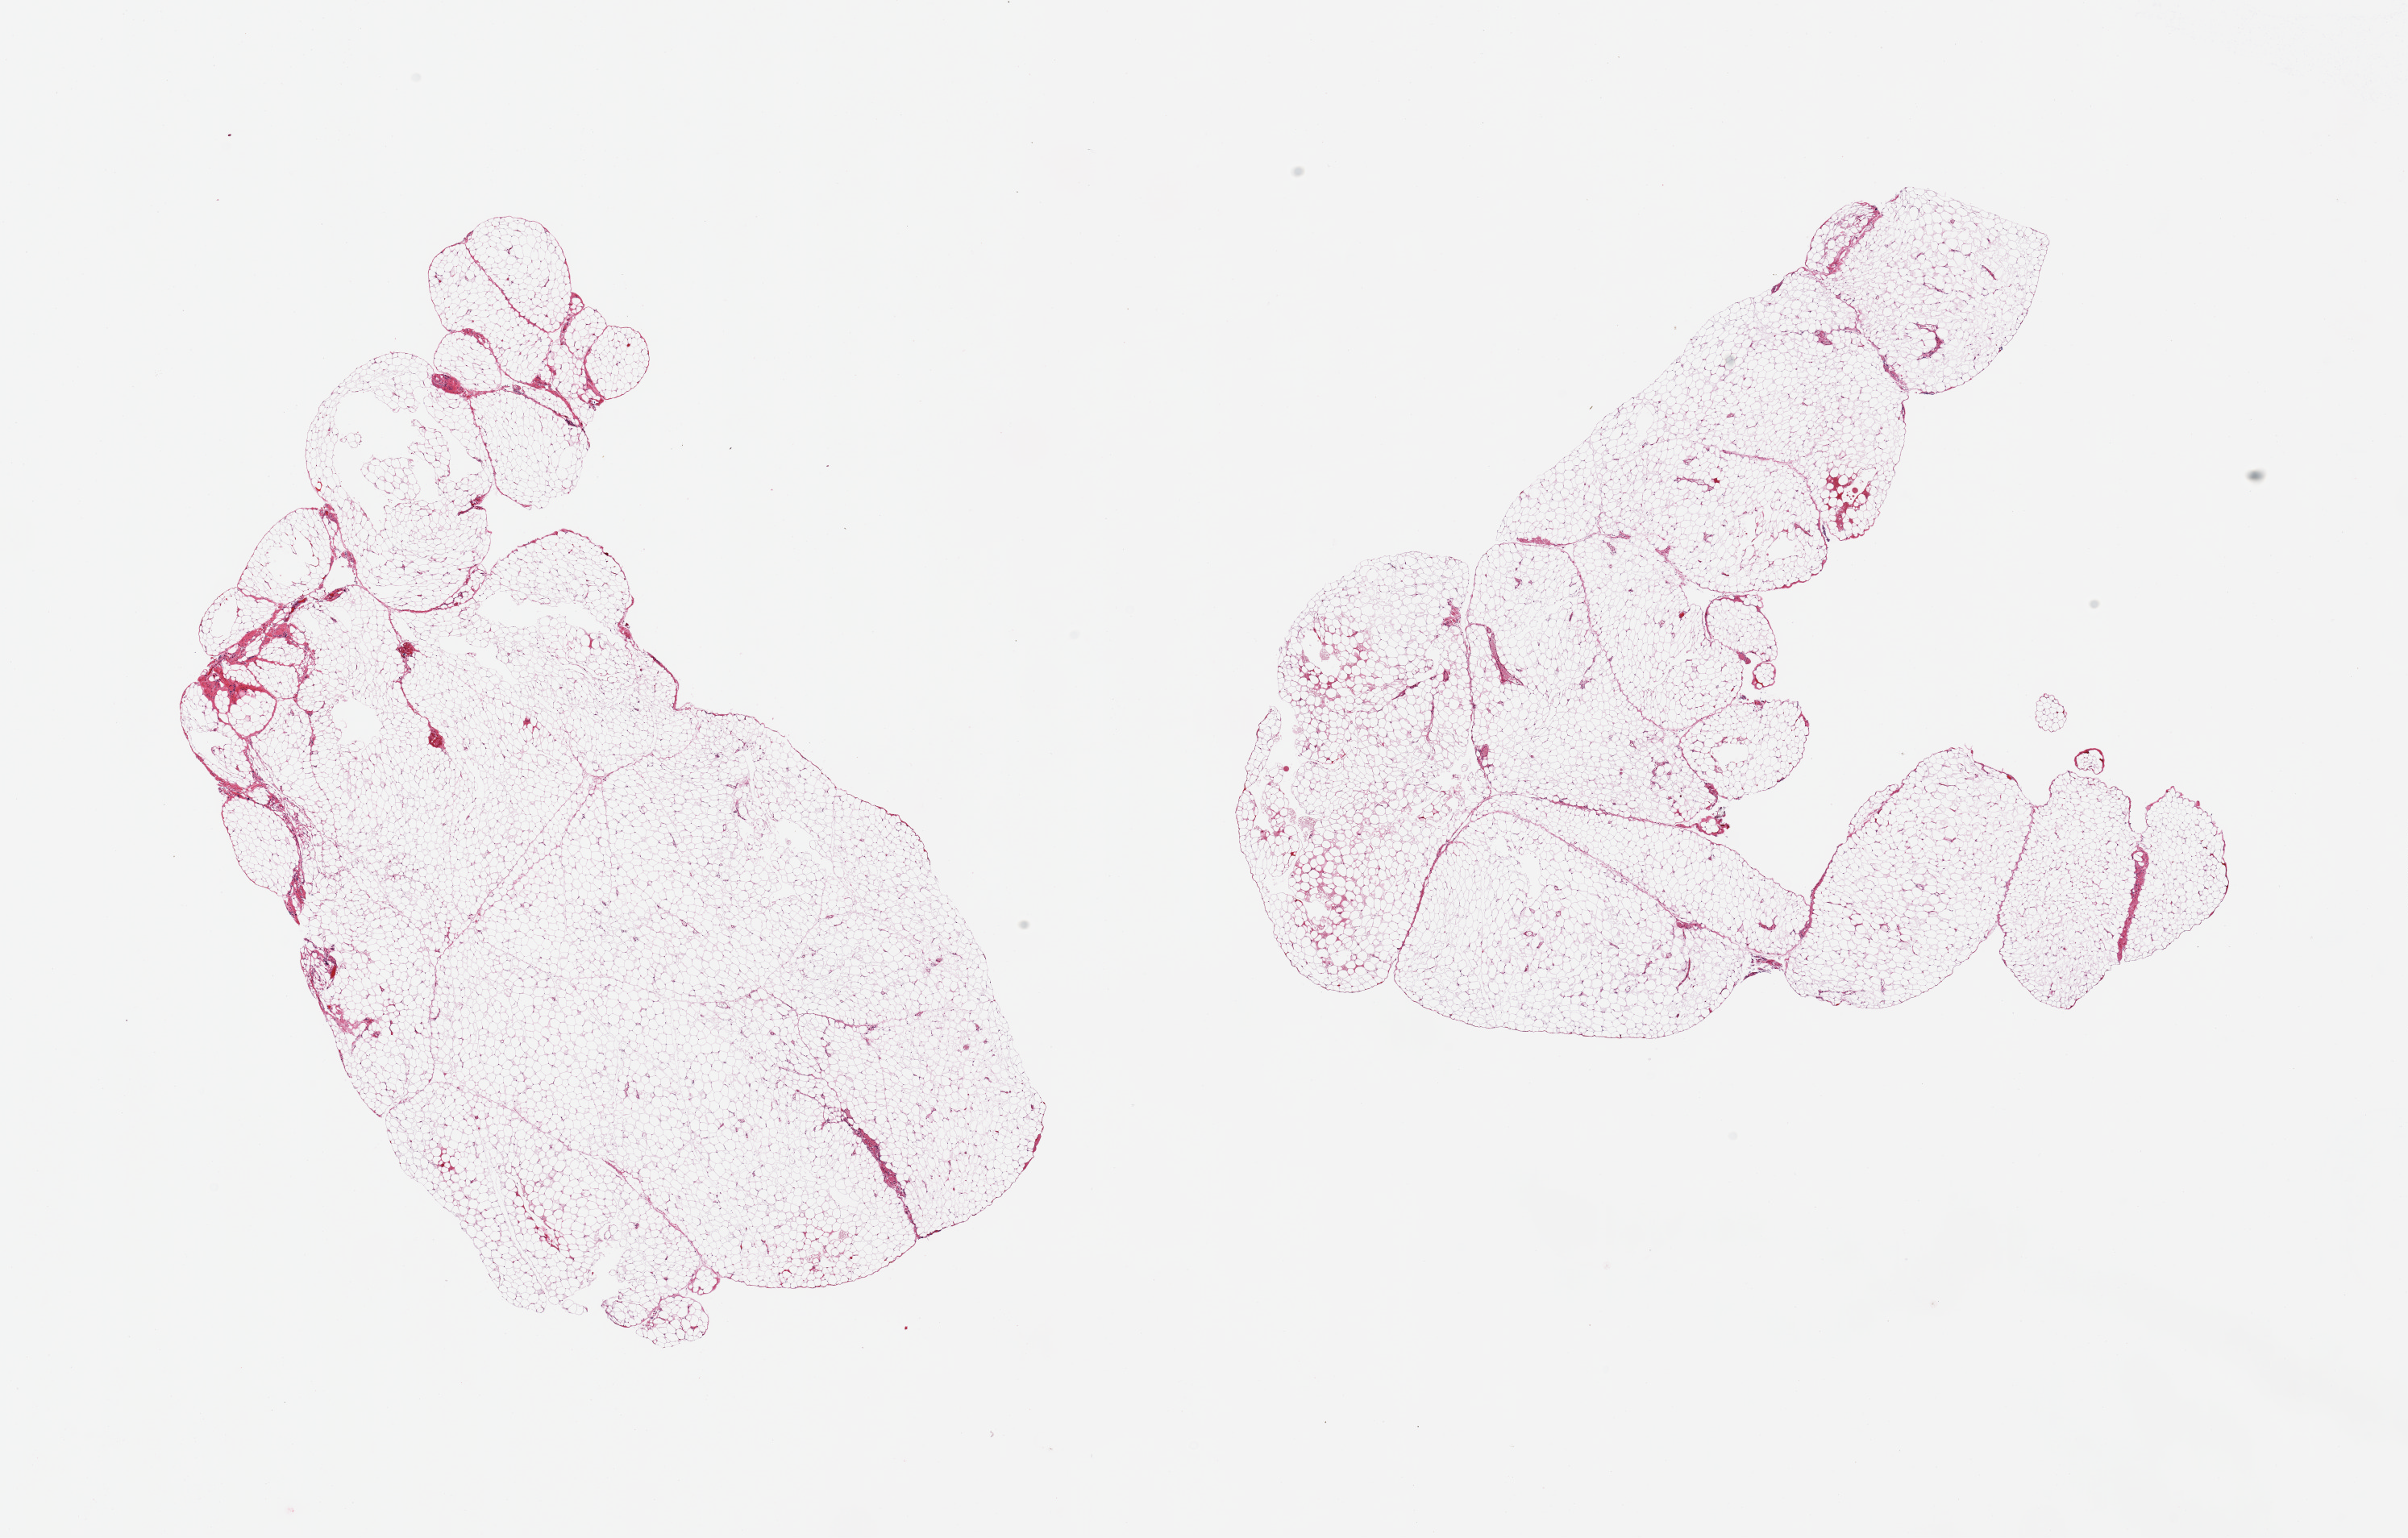
Whole-slide image, hematoxylin and eosin (H&E) stain, low-resolution overview of the scanned area, about 23.6 x 15.1 mm; PAXgene-fixed, paraffin-embedded tissue; target tissue: omentum; donor tissue sample. Donor sex: male.
Pathologist's review note for this sample: 2 pieces; lobulated adipose tissue; congestion.